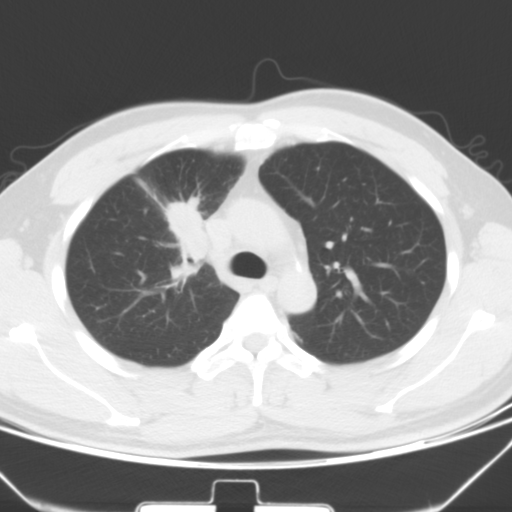
Chest CT, one axial slice; position 42 of 60 along the scan axis; 120 kVp; lung window (W 1500 / L -600 HU); 5 mm slice thickness; 512 × 512 image matrix, field of view 337 × 337 mm. Patient: male, 35 years. Case-level facts recorded for this patient, not image findings: clinical TNM (as recorded): T1c N1 M1b.
Structures marked on this image (bounding box drawn by a radiologist):
- lung tumour (recorded histology: adenocarcinoma): bounding box [x1, y1, x2, y2] px = [160, 195, 213, 264]